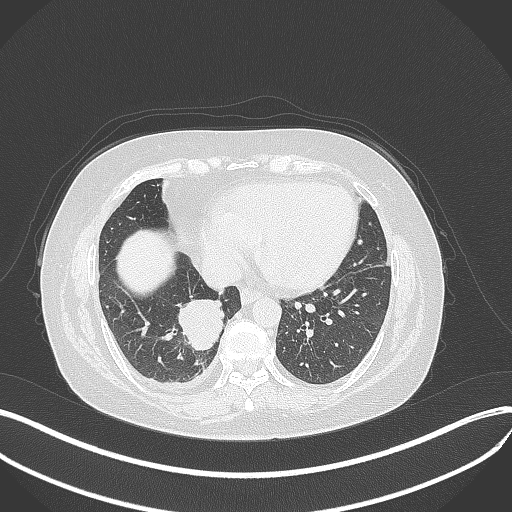
Chest CT, one axial slice; position 121 of 381 along the scan axis; 120 kVp; lung window (W 1500 / L -600 HU); 512 × 512 image matrix, field of view 400 × 400 mm. Female patient, age 56 years. Case-level facts recorded for this patient, not image findings: clinical TNM (as recorded): T2b N1 M0; histopathological grade: G3.
Structures marked on this image (rectangle marked by the reading radiologist):
- lung tumour (recorded histology: small cell carcinoma): bounding box [x1, y1, x2, y2] px = [176, 297, 228, 355]